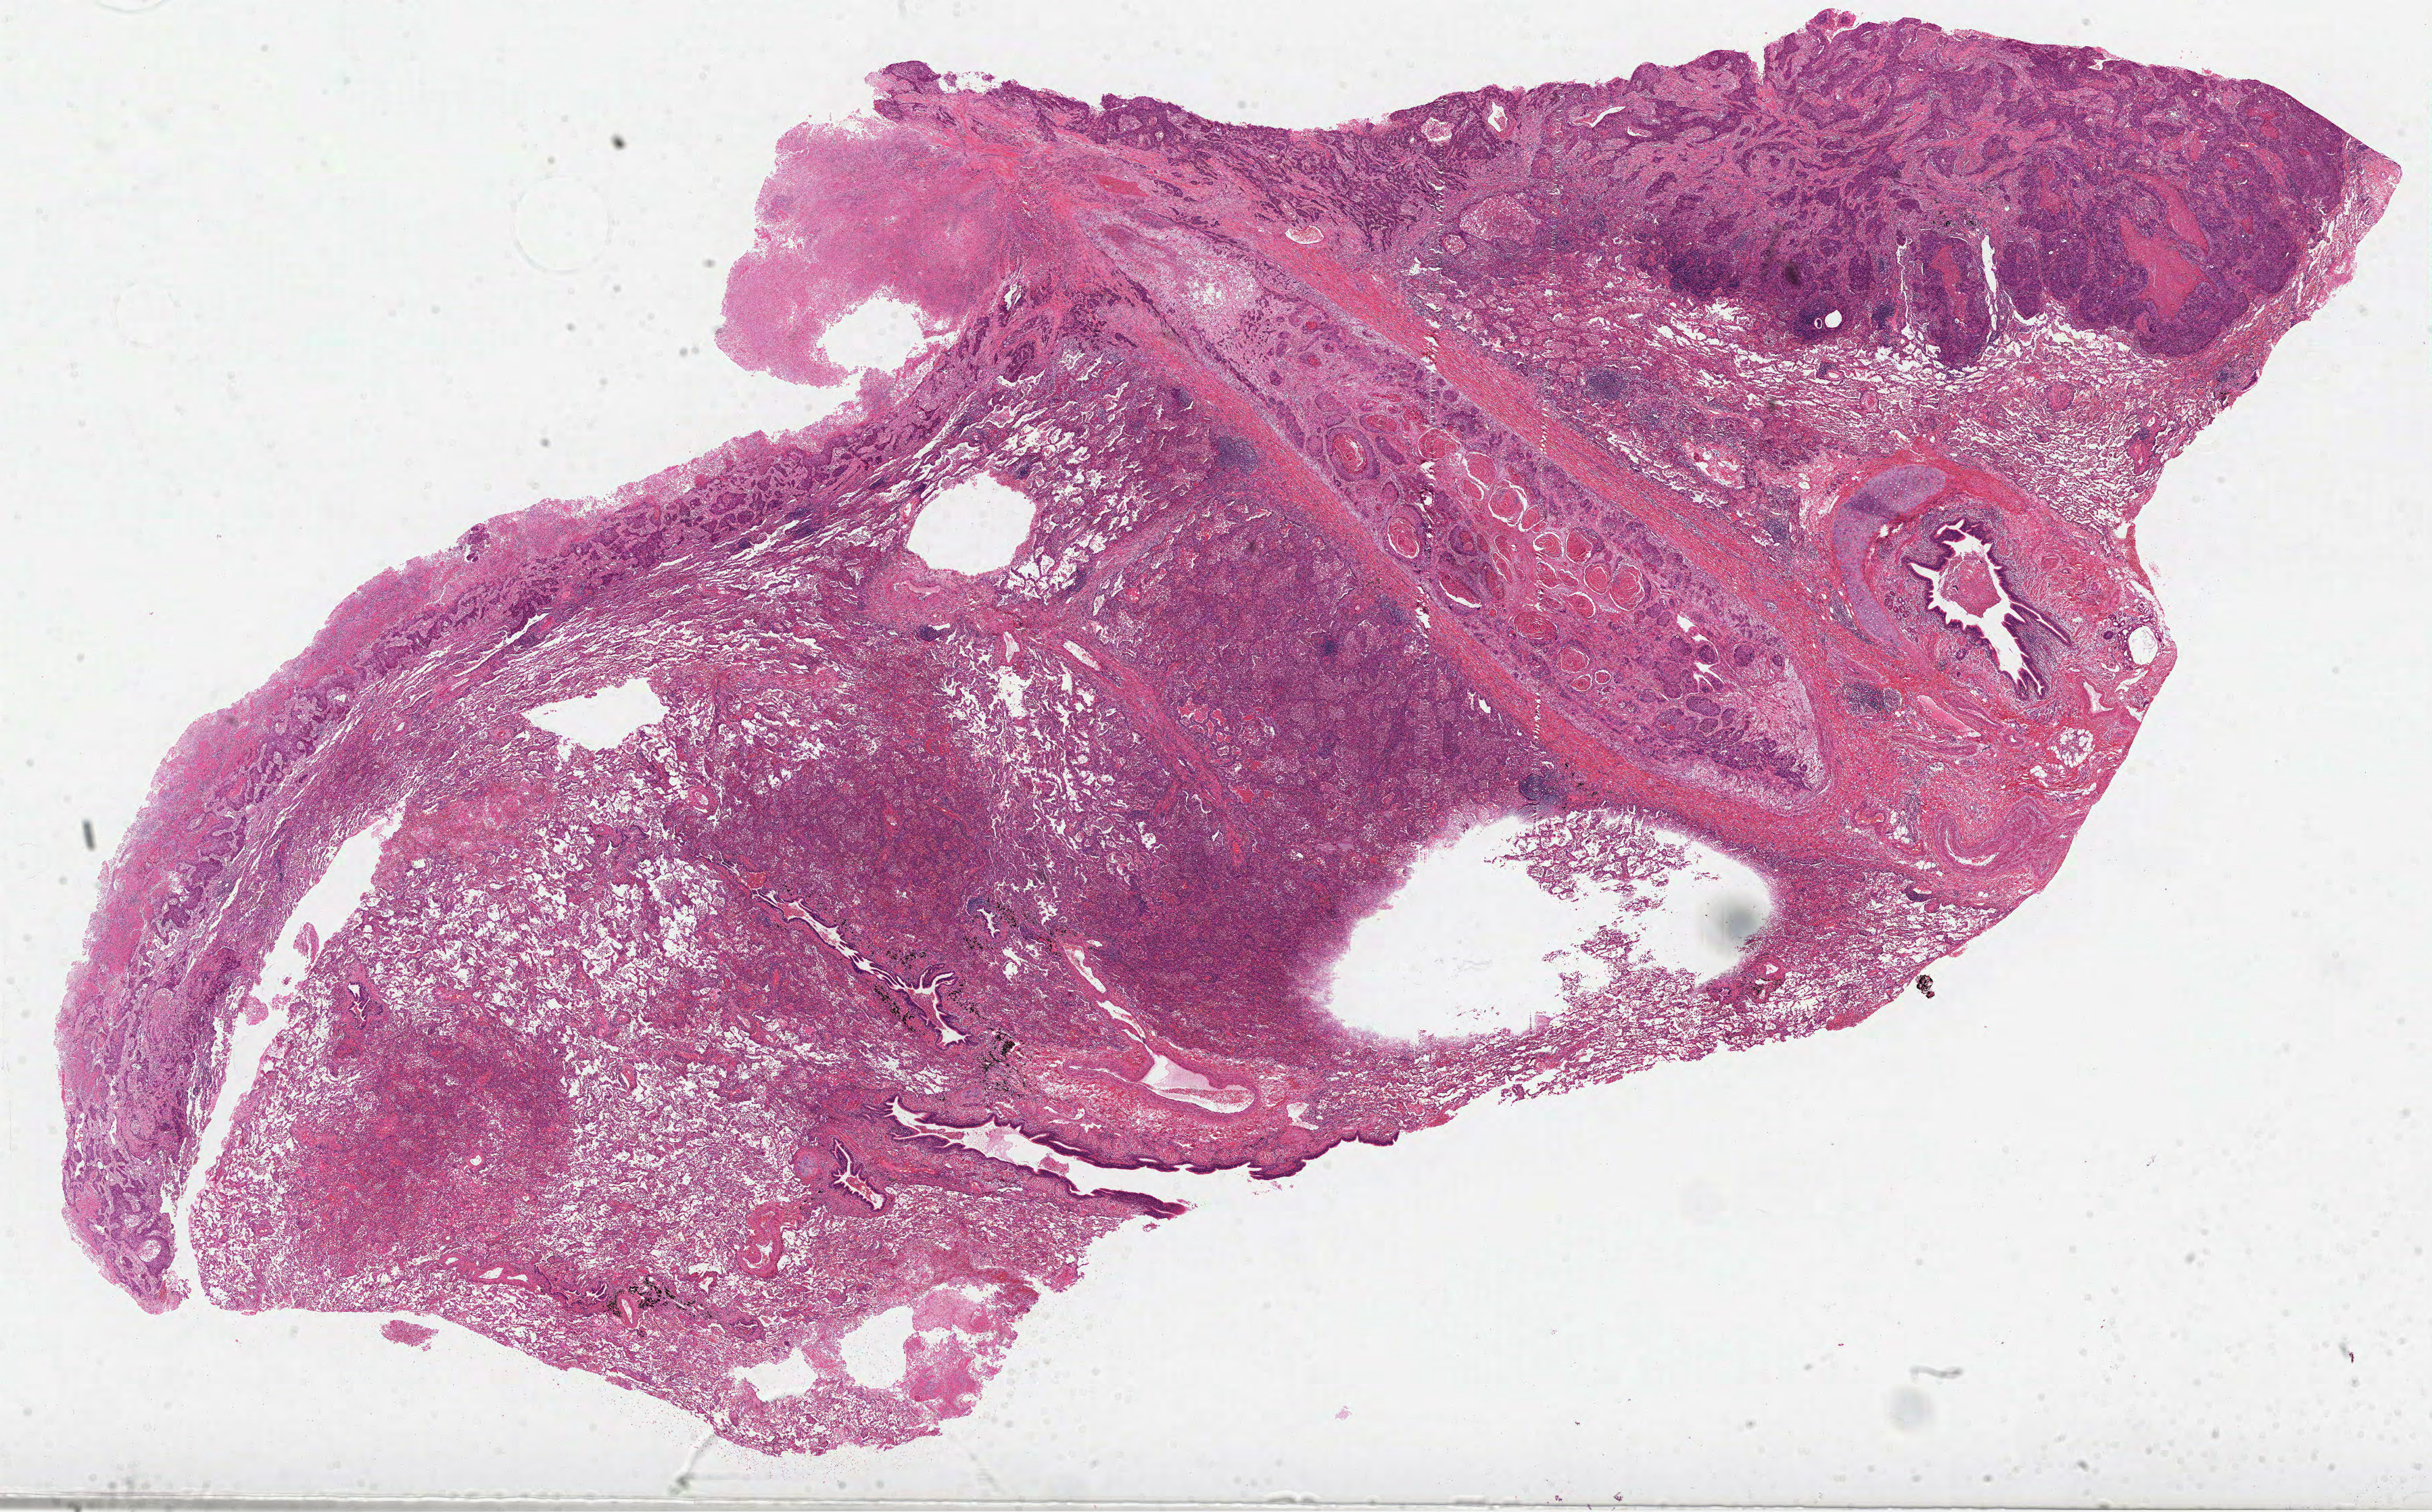
H&E-stained whole-slide image, low-resolution overview of the scanned area, about 29.0 x 18.0 mm; formalin-fixed paraffin-embedded (FFPE) diagnostic section; primary tumour sample from the lung. Male patient; age at initial diagnosis 67 years.
TNM: T2 N0 M0. AJCC pathologic stage: IB (6th edition). Histologic diagnosis: Squamous cell carcinoma, NOS (lower lobe, lung).